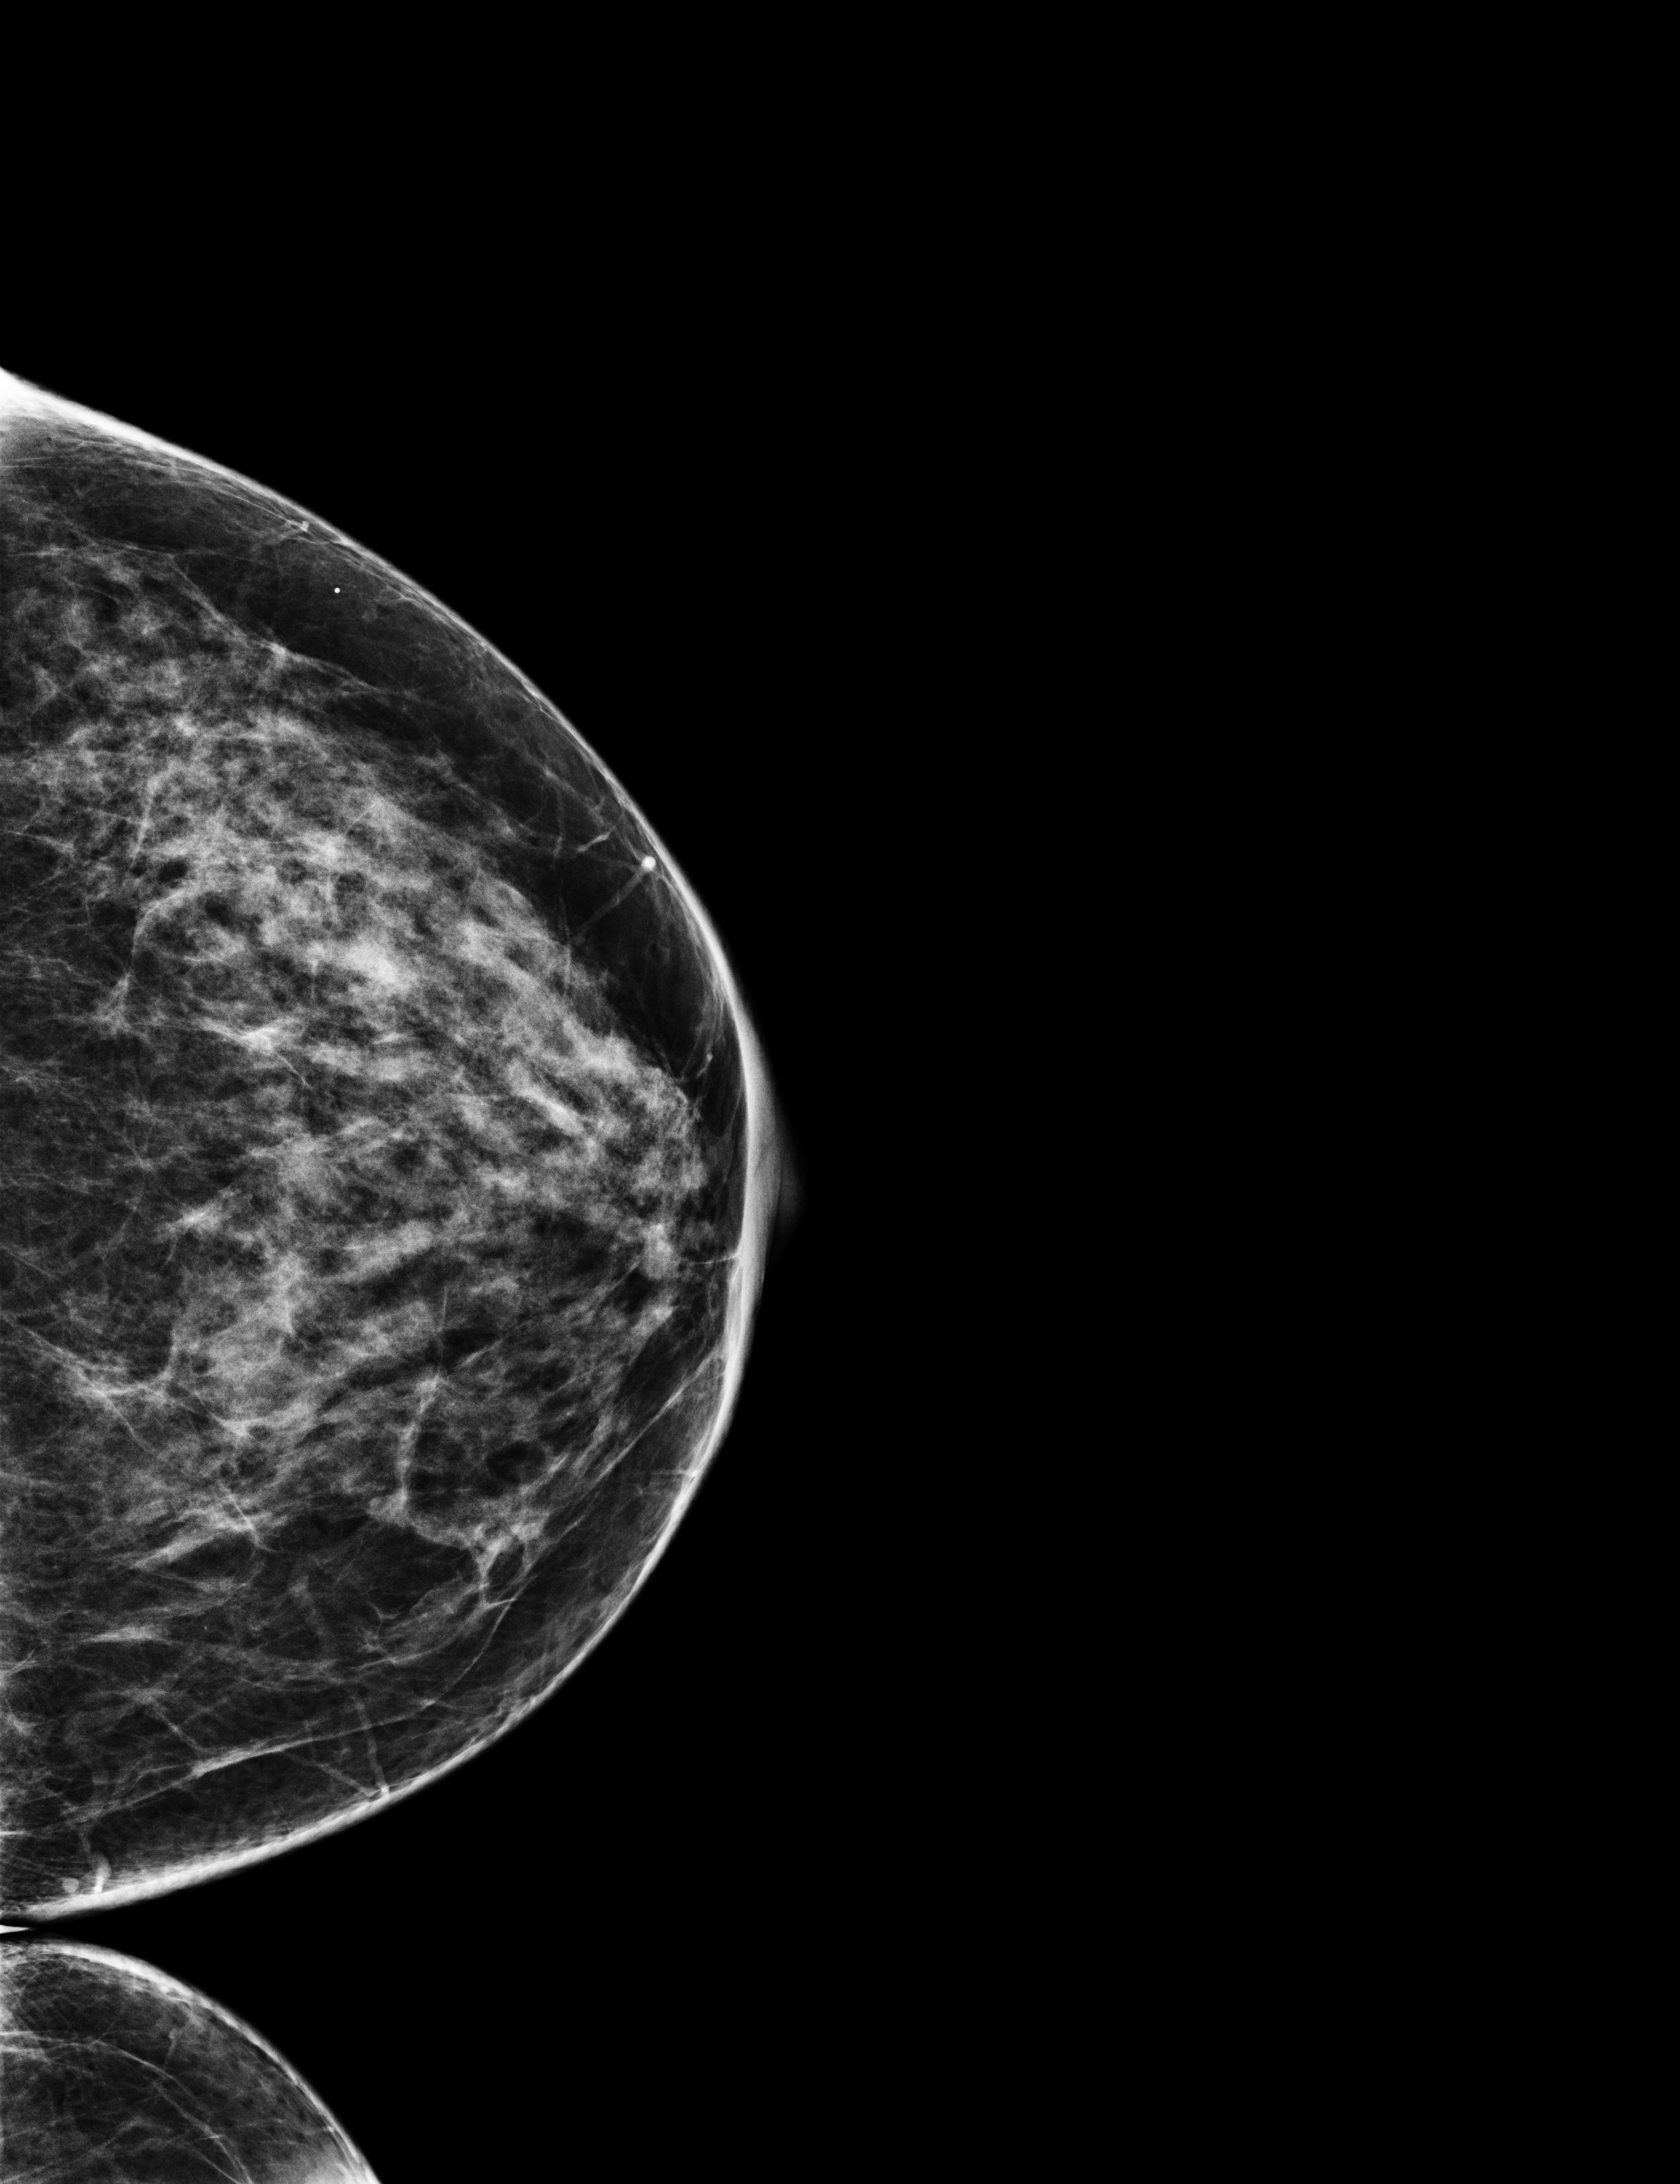
Full-field digital mammogram (FFDM); left breast; craniocaudal (CC) view; annual screening mammography examination; compressed breast thickness 53 mm. Patient: female, 60 years.
- BI-RADS breast density category at the screening exam (both breasts, scale 1–4): 3
- final BI-RADS category for the screening round (tomosynthesis exam, both breasts): category 1
- recall: no recall after this screen